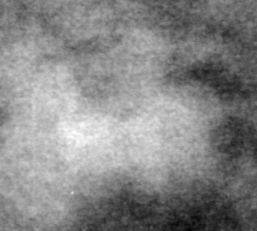
Cropped region of a digitized screen-film mammogram centred on a radiologist-marked abnormality; right breast; CC view; BI-RADS breast density category 3 (scale 1–4).
Marked abnormality: mass, shape lobulated, margins ill defined; BI-RADS assessment category 4; subtlety rating 1 on a 1 (subtle) to 5 (obvious) scale; pathology result (as recorded, not read from the image): malignant.